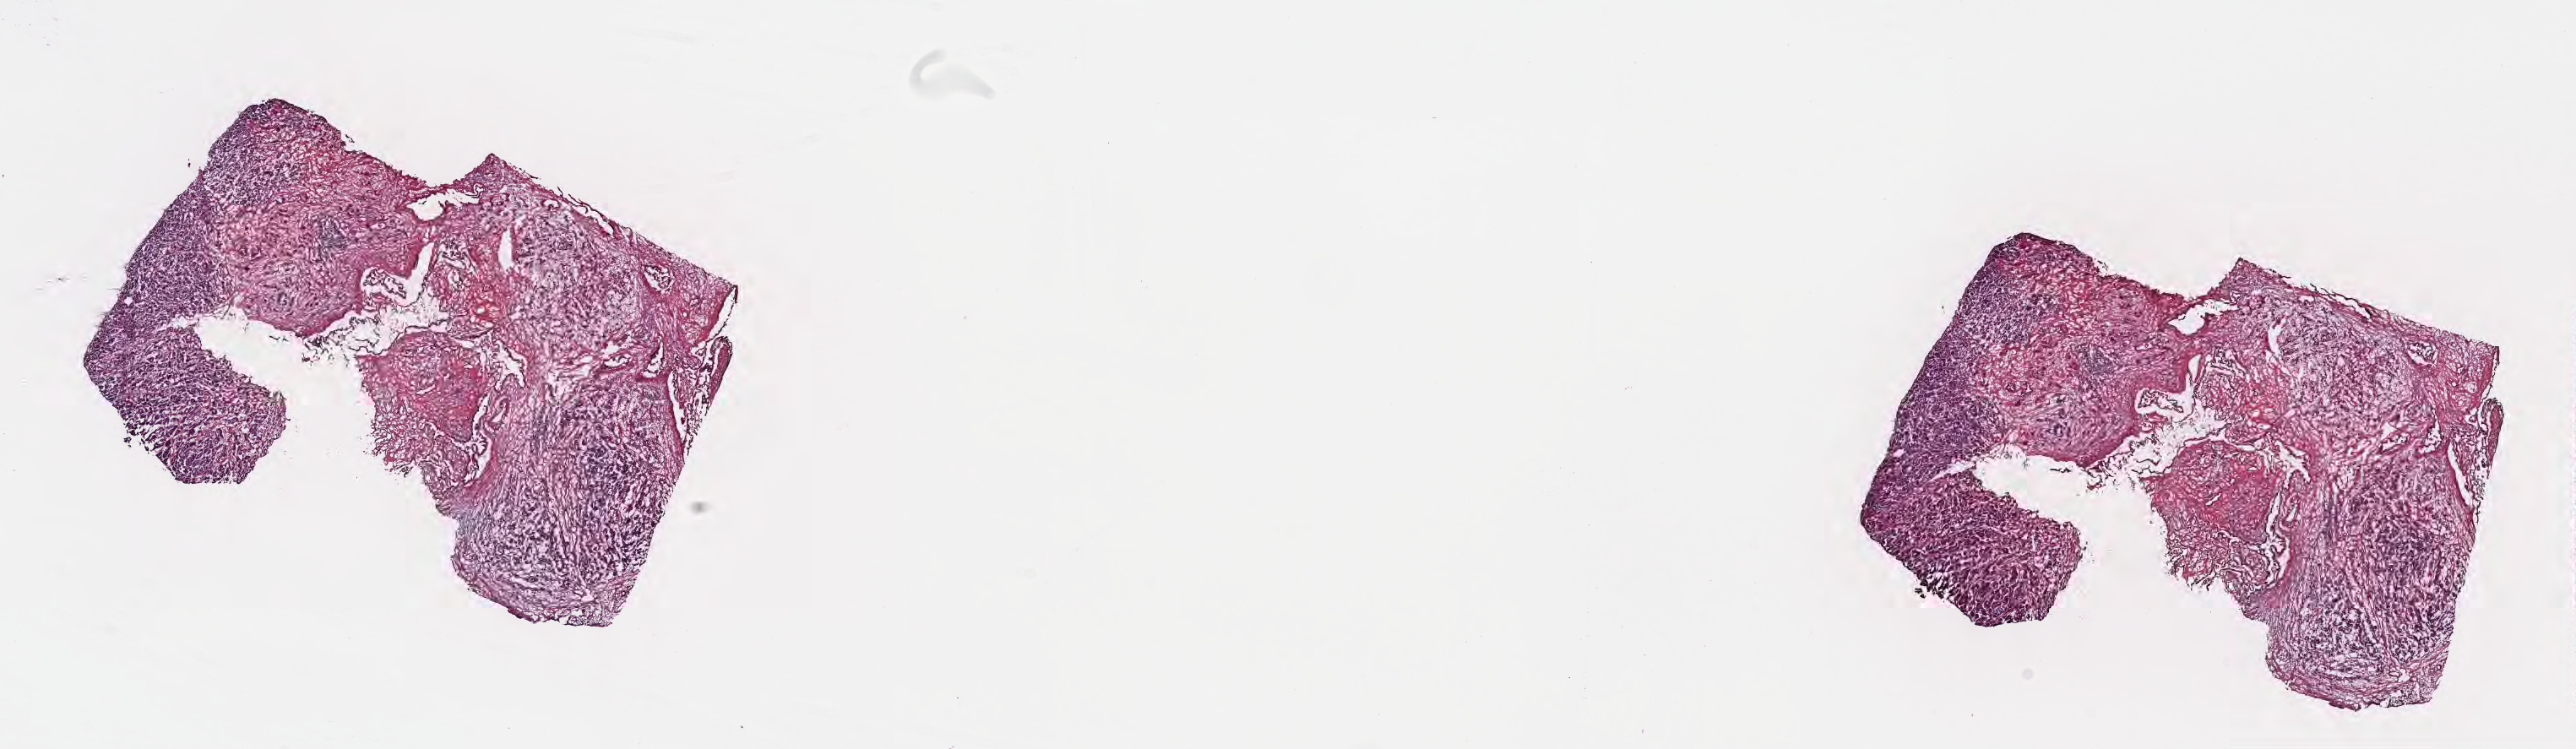
Haematoxylin and eosin whole-slide image, shown as a low-resolution overview of the whole scanned area (about 24.6 x 7.2 mm), cryosection, primary tumor, anatomic site: head of pancreas. Patient: female, age at initial diagnosis 60 years. Tumor grade: G2 (moderately differentiated). Slide review estimates, as recorded: tumor cells 40%, tumor nuclei 50%, stromal cells 50%, necrosis 0%, normal cells 10%. Inflammatory infiltration, as recorded: lymphocyte infiltration 0%, monocyte infiltration 0%, neutrophil infiltration 0%.
Section: bottom of the tissue portion. AJCC pathologic stage: Stage III. Diagnosis: Infiltrating duct carcinoma, NOS.